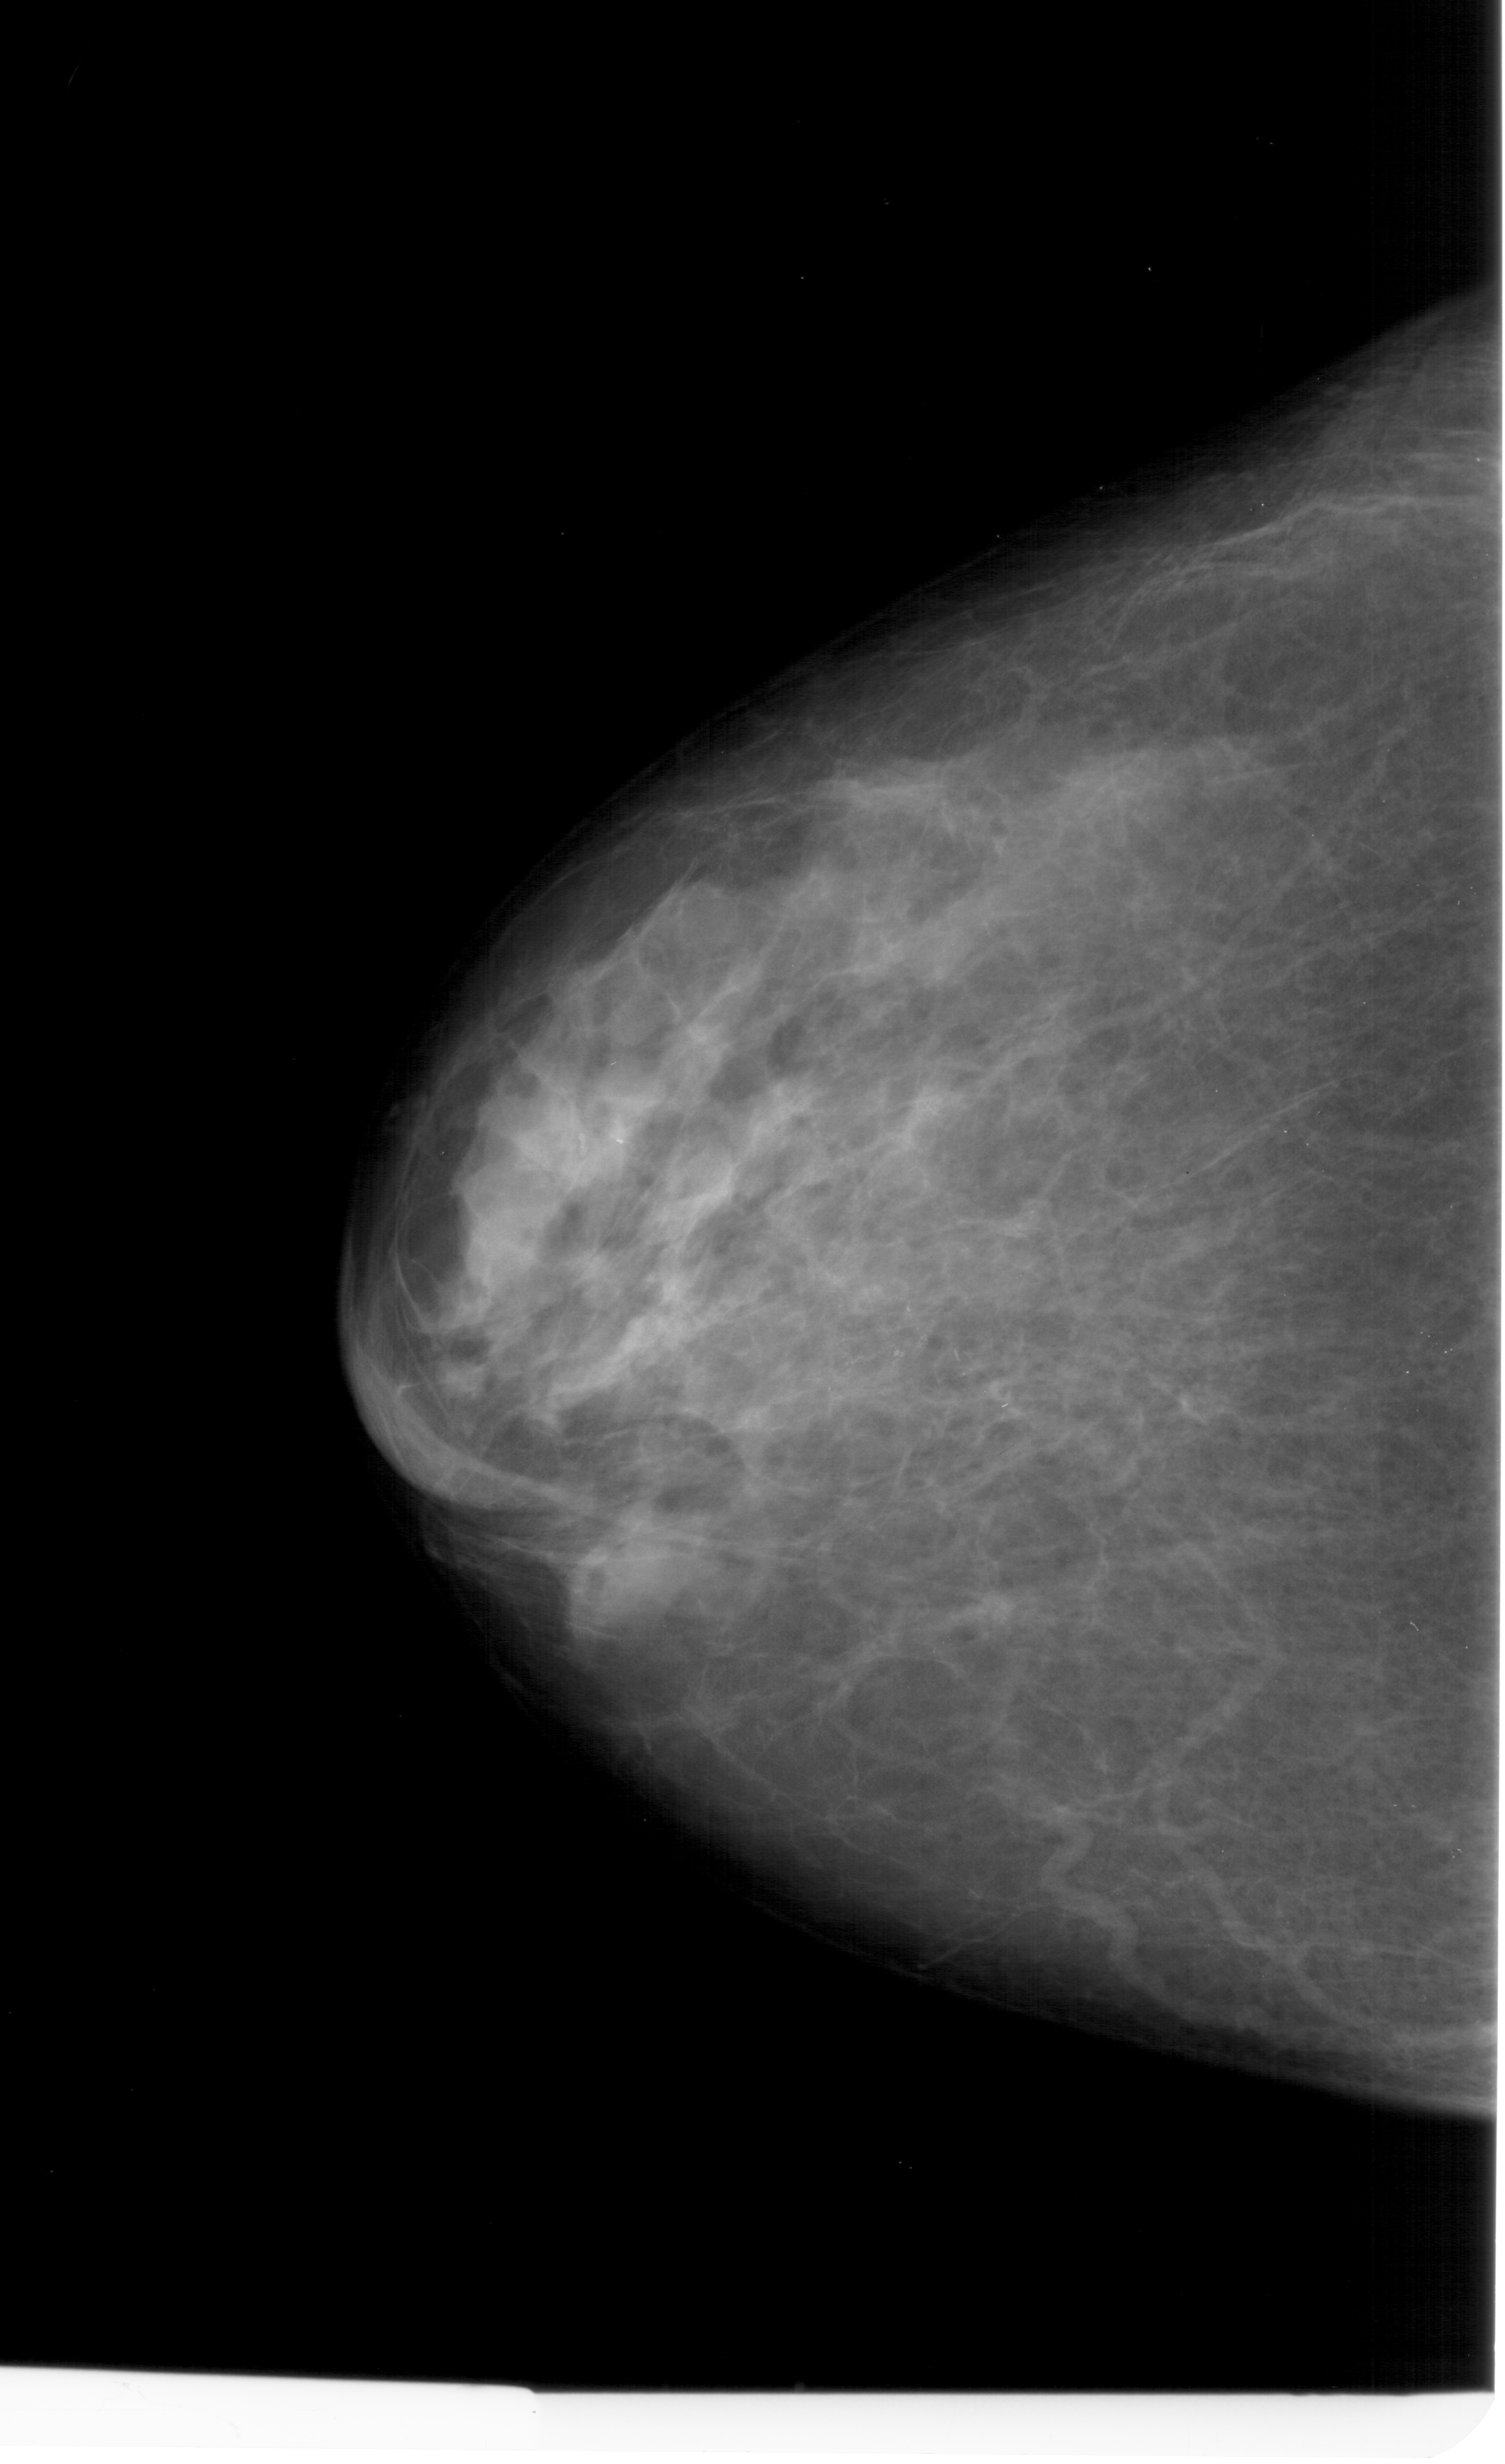
Scanned film-screen mammogram; left breast; craniocaudal (CC) view; breast composition: heterogeneously dense (BI-RADS density category 3 of 4); 1505 × 2464 image matrix.
Marked abnormalities (boxes around the expert regions of interest):
- calcifications, morphology pleomorphic, distribution clustered; BI-RADS assessment category 4; pathology (as recorded): benign: bounding box (x1, y1, x2, y2) in pixels: (746, 1234, 1039, 1463)